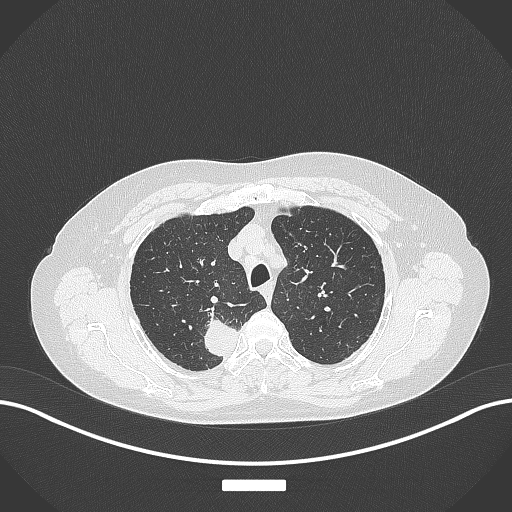
Chest CT, one axial slice; slice 308 of 357 in the series (ordered by position); 120 kVp; lung window (W 1500 / L -600 HU); 512 × 512 image matrix. Female patient, age 62 years. From the clinical record (not read from this slice): clinical TNM (as recorded): T1c N1 M0.
Structures marked on this image (rectangle marked by the reading radiologist):
- lung tumour (recorded histology: squamous cell carcinoma): bounding box [x1, y1, x2, y2] px = [196, 310, 238, 361]